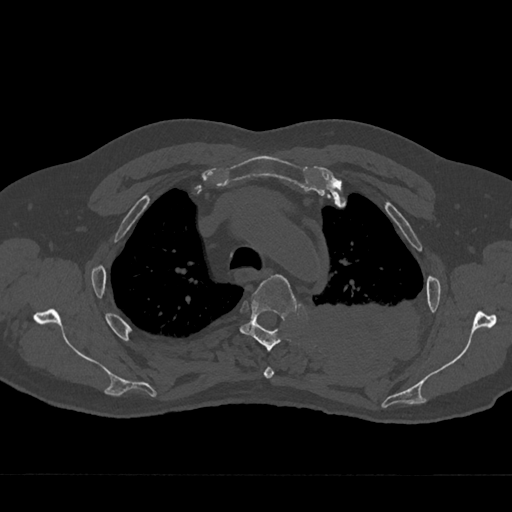
CT including the spine, one axial slice; position 527 of 797 along the scan axis; reconstruction kernel Br40s/3; bone window (W 1800 / L 400 HU); 0.5 mm slice thickness; 512 × 512 image matrix, field of view 377 × 377 mm. Patient: male, 75 years. From the clinical record (not read from this slice): primary cancer: renal.
Outlined on this slice (semi-automatic segmentation, software-assisted and operator-edited):
- T3 vertebra: bounding box [x1, y1, x2, y2] px = [264, 367, 275, 379]
- T4 vertebra: [239, 275, 297, 351]